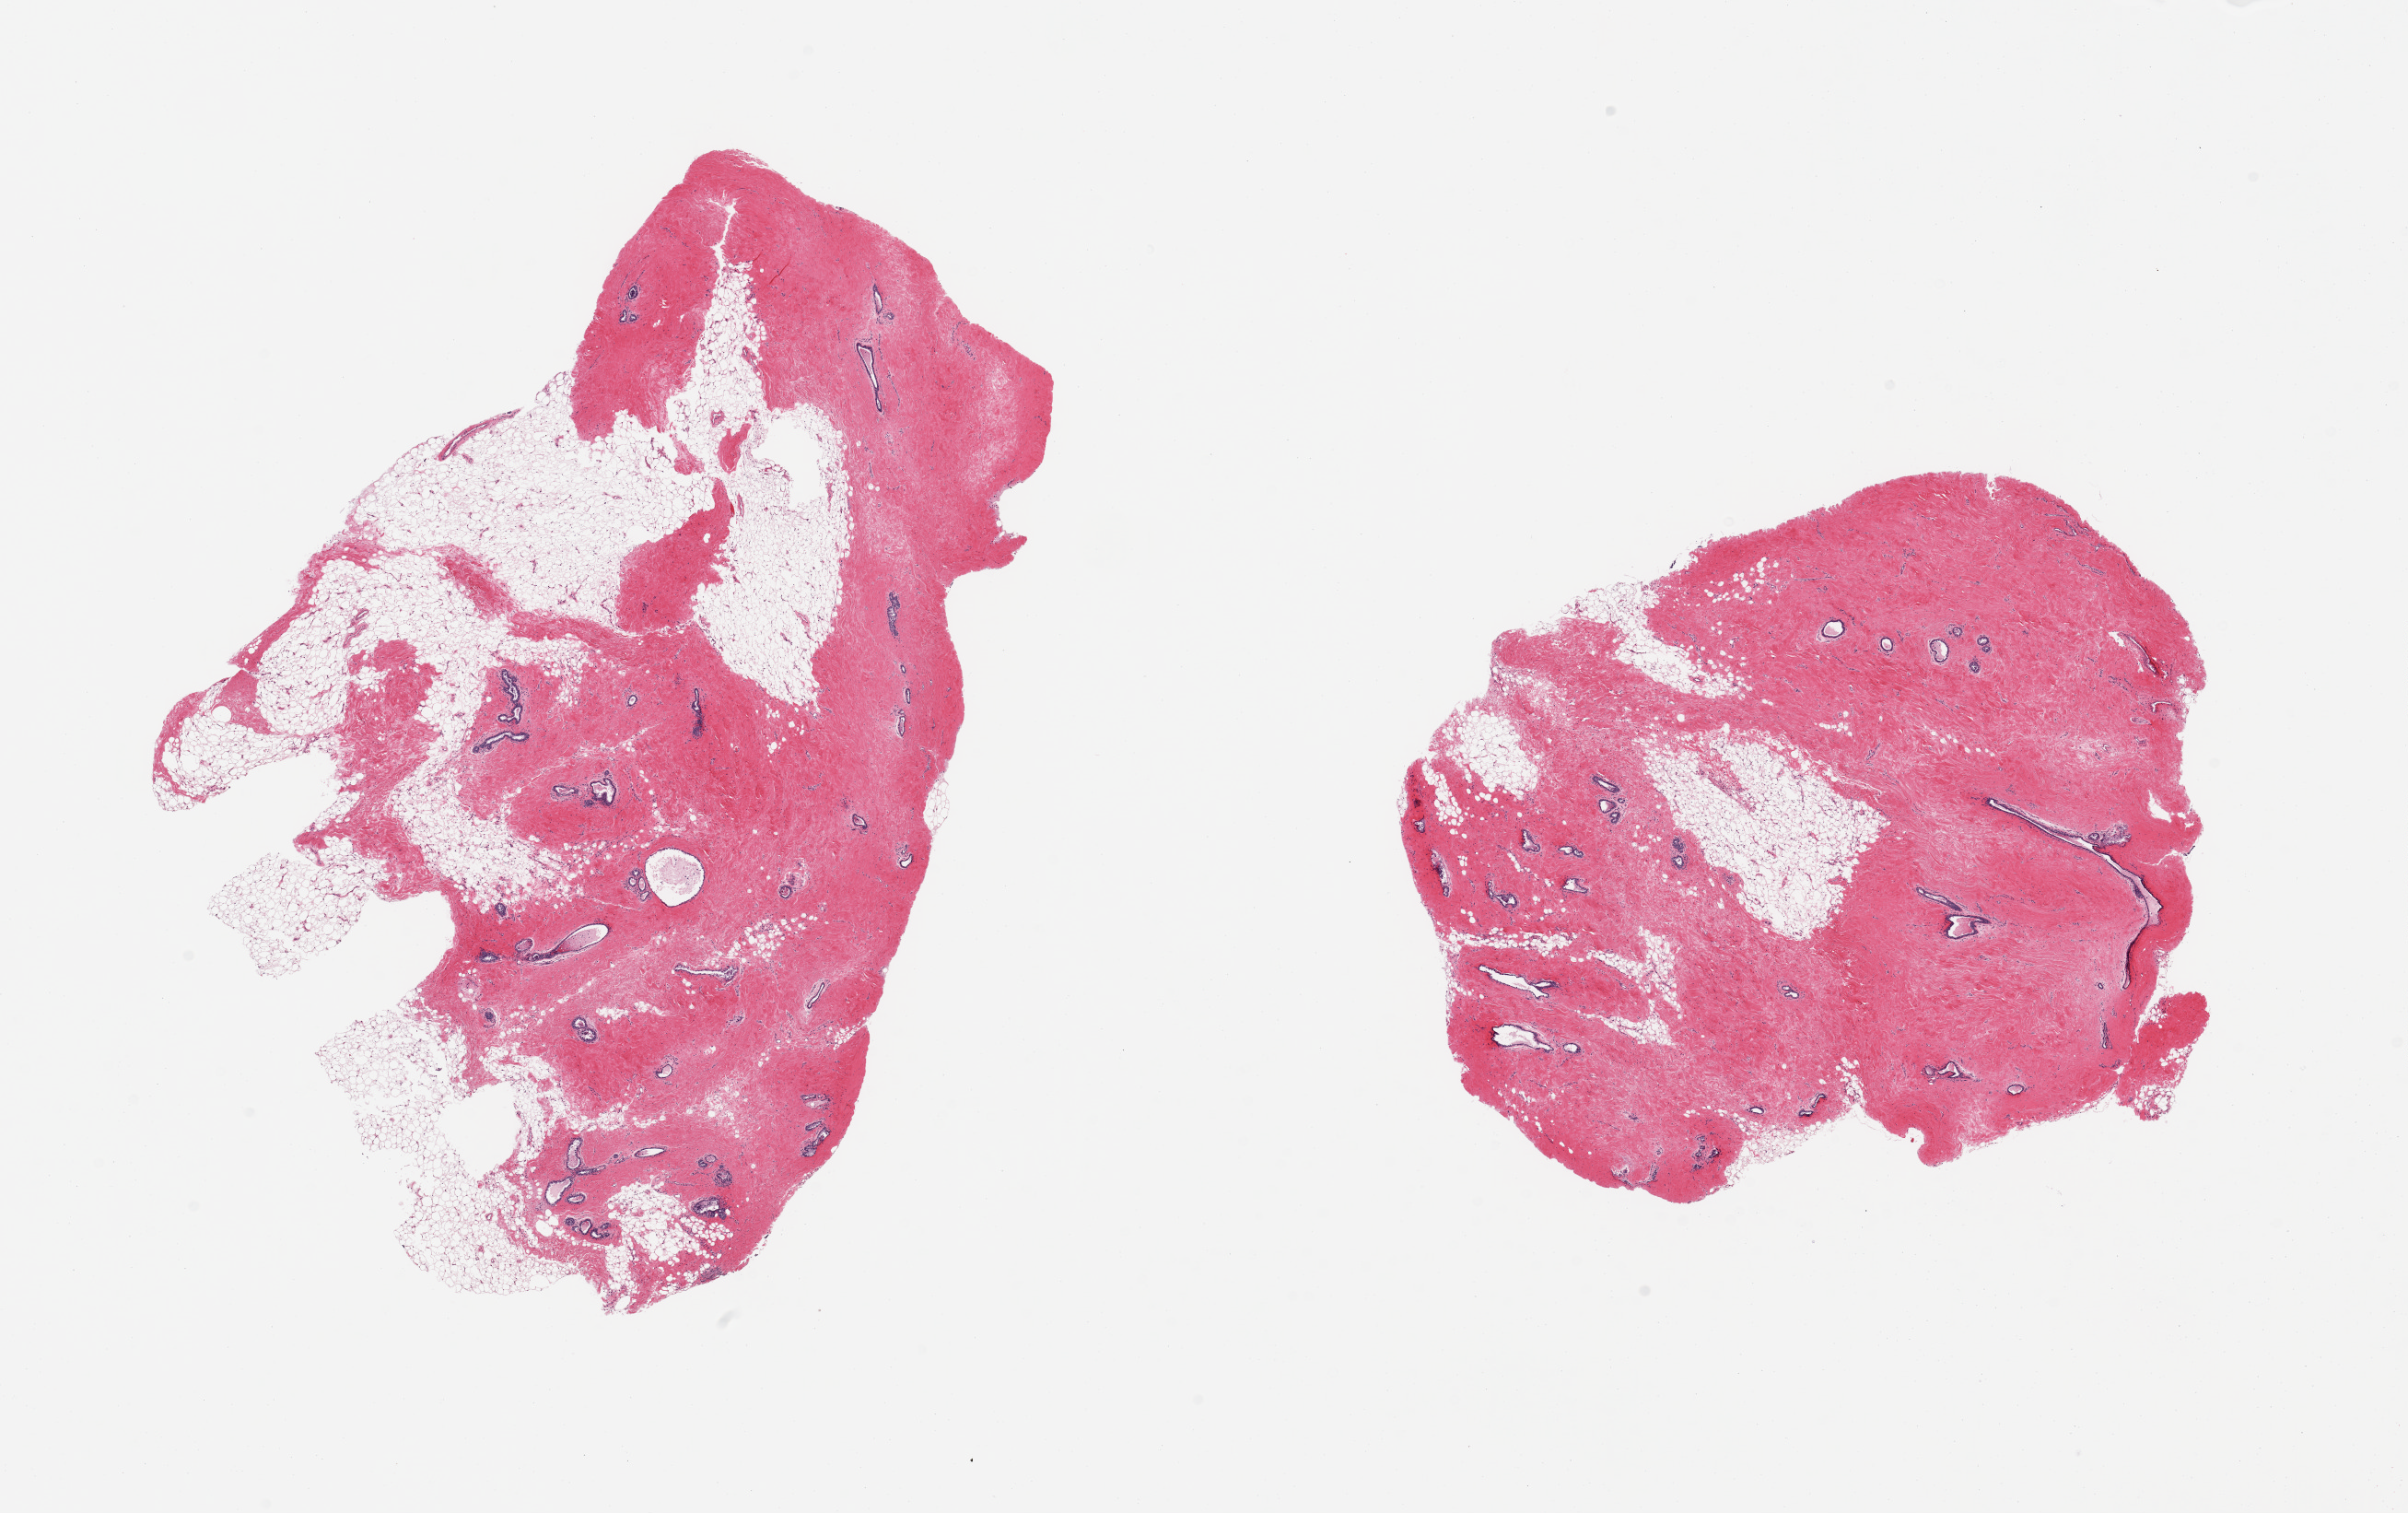
Whole-slide image, H&E stain, low-resolution overview of the scanned area, about 20.7 x 13.0 mm. PAXgene-fixed paraffin-embedded (PFPE) section. Target tissue: breast. Tissue donor sample.
- review note (as recorded): 2 pieces, gynecosmastoid stromal/ductal hyperplasia, rep ductal elements